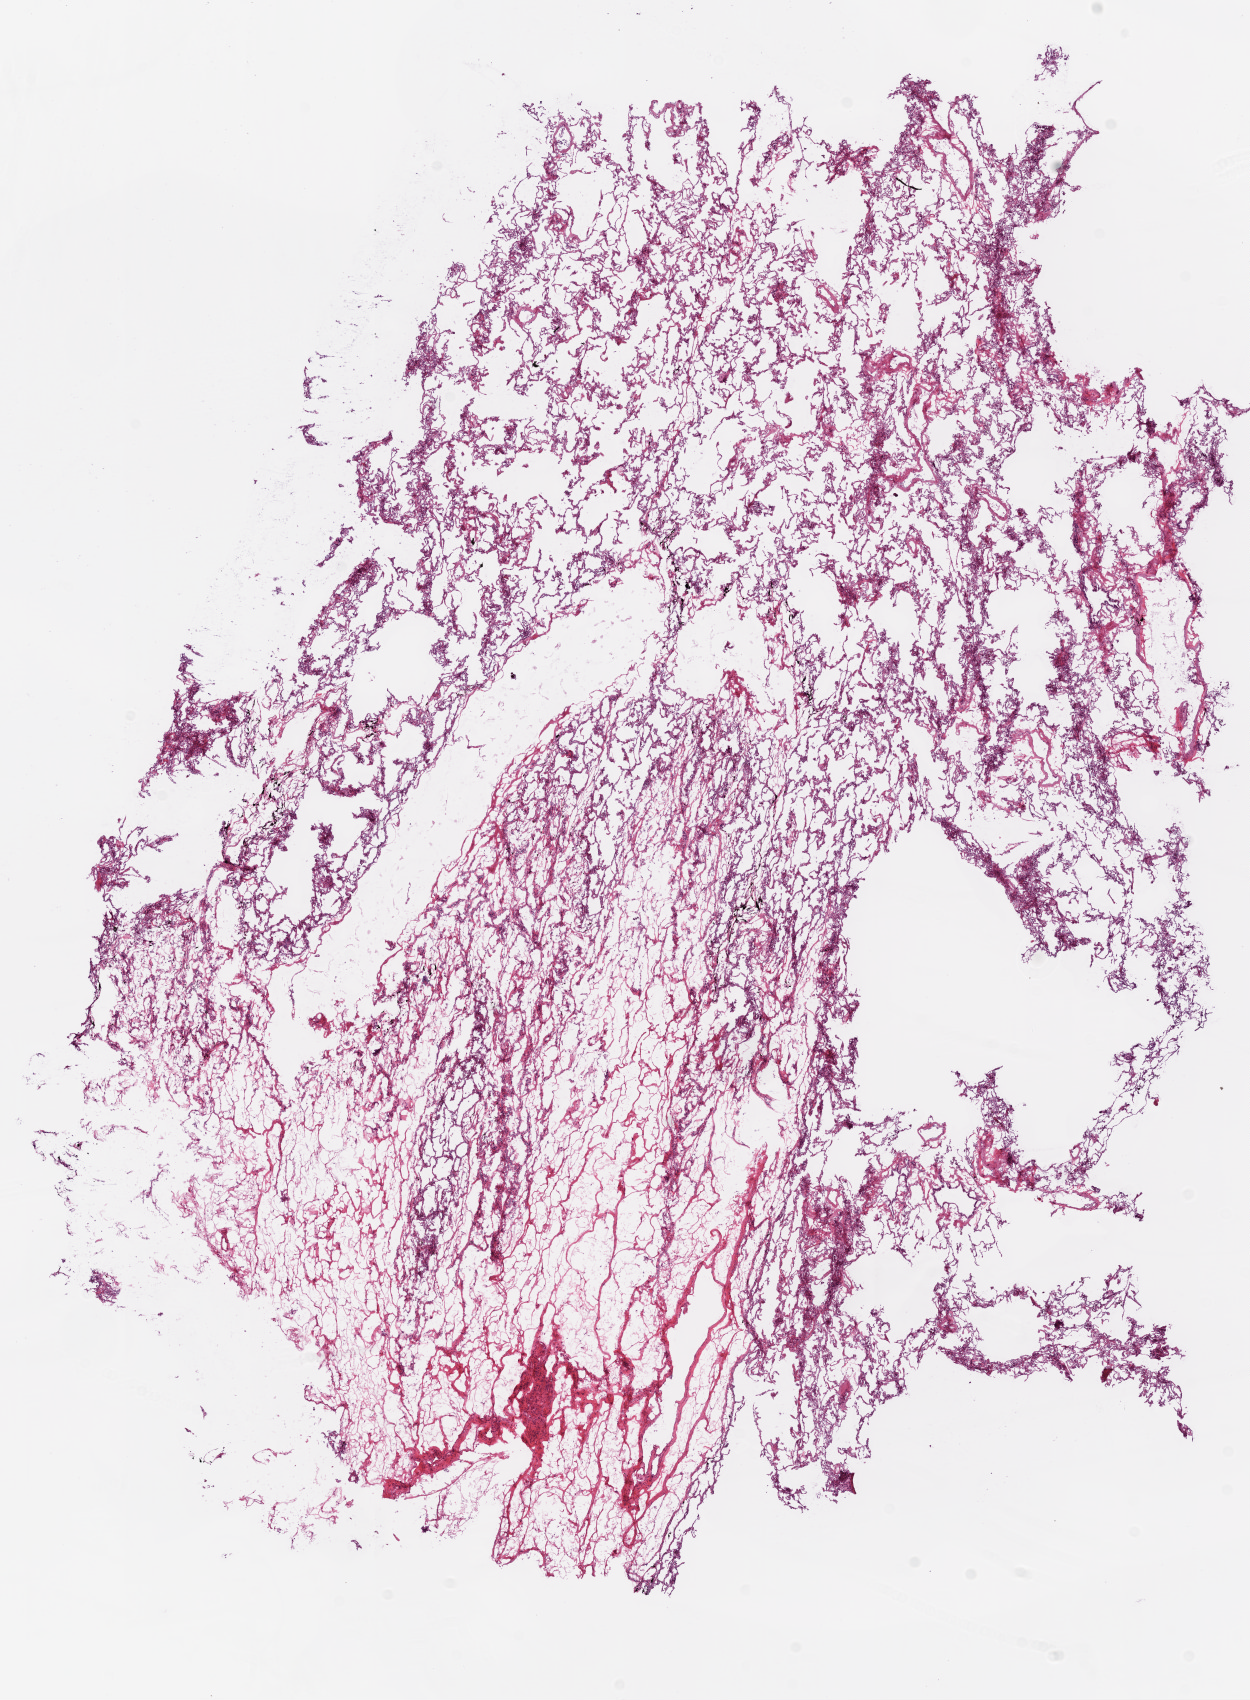
Digitized H&E tissue section (whole slide), shown as a low-resolution overview of the whole scanned area (about 10.0 x 13.6 mm, from a 20x scan), frozen section, sample: solid tissue normal (non-tumour tissue), lung. Female patient; age at initial diagnosis 81 years.
This section: solid tissue normal (non-tumour) sample from the same patient. Patient diagnosis: Squamous cell carcinoma, NOS (lower lobe, lung).